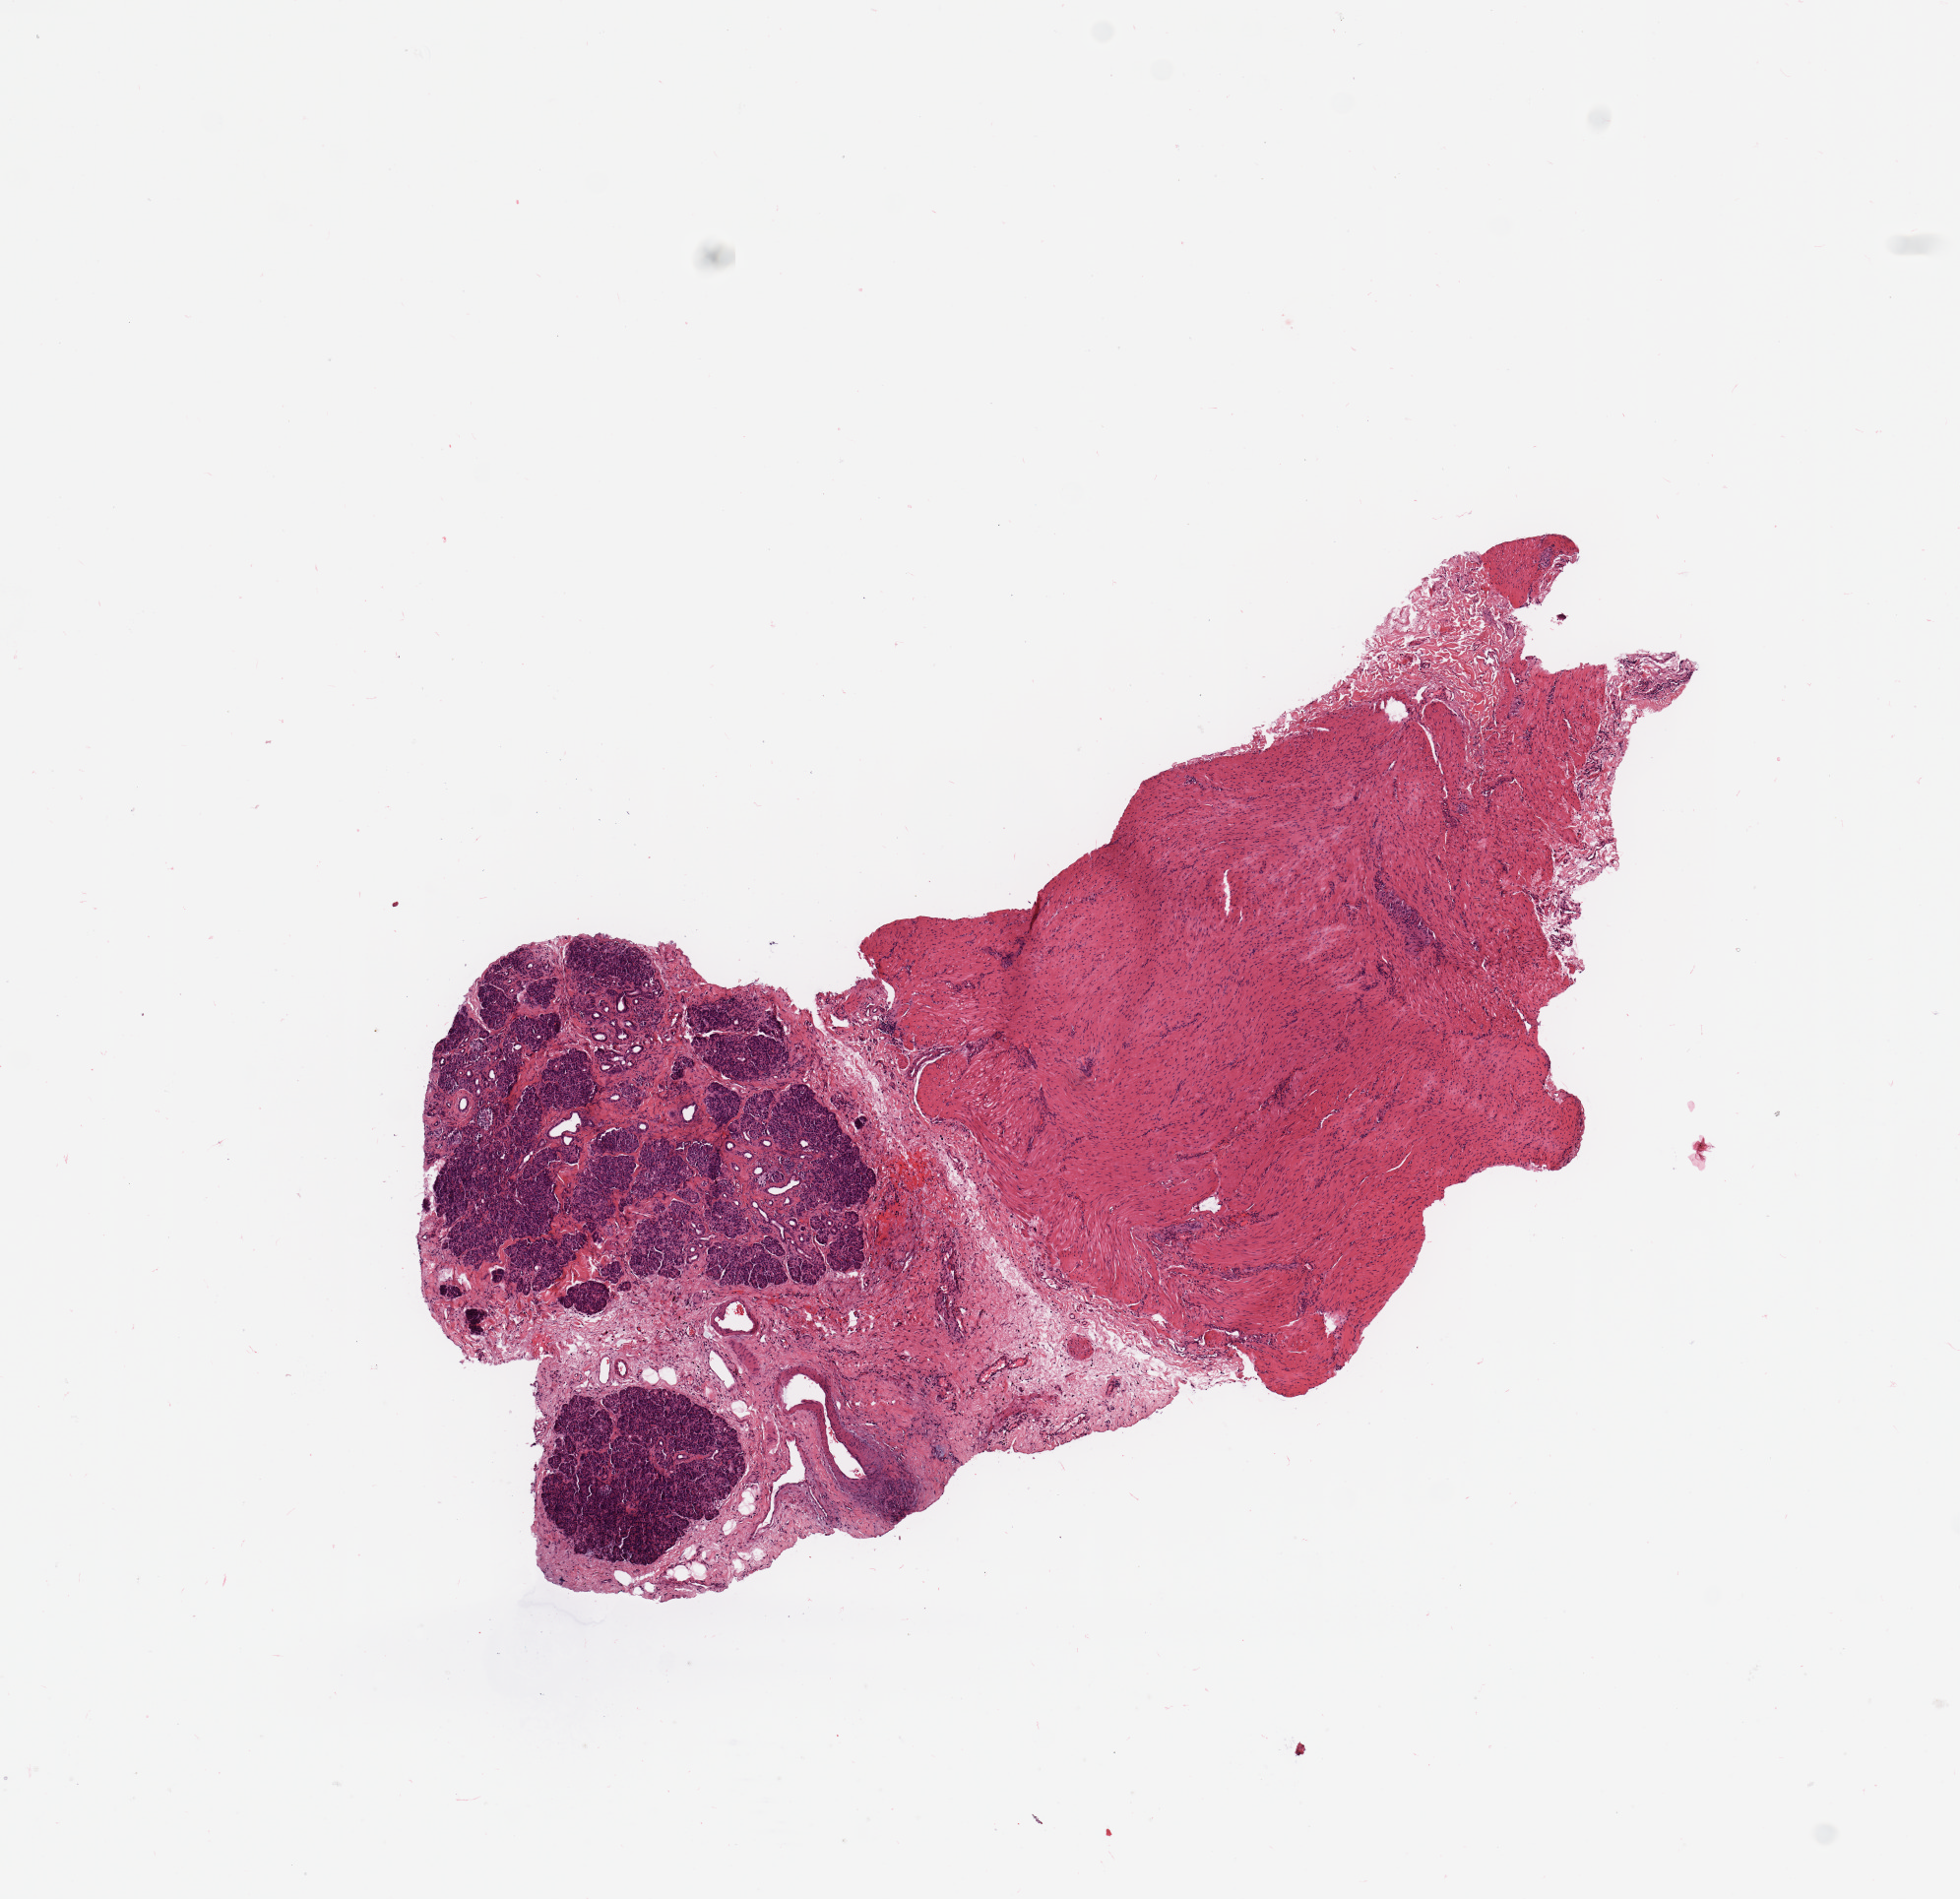
Whole-slide histology image, Hematoxylin and eosin (H&E) stained, shown as a low-resolution overview of the whole scanned area (about 7.9 x 7.6 mm), pancreas, normal (non-tumour) tissue. Male, 66 y/o.
This section: normal (non-tumour) tissue from the same patient. Patient diagnosis: Infiltrating duct carcinoma, NOS.